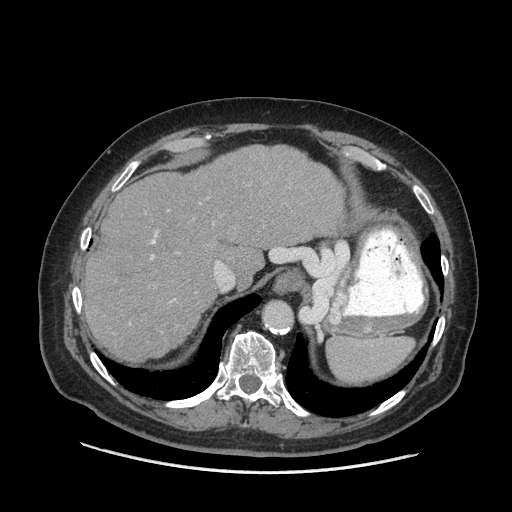
Contrast-enhanced abdominal CT (liver protocol), one axial slice. Soft-tissue window (W 400 / L 40 HU). 2.5 mm slice thickness. 512 × 512 image matrix, field of view 420 × 420 mm. Case-level facts recorded for this patient, not image findings: diagnosis: hepatocellular carcinoma (patient treated with transarterial chemoembolisation; whether this scan precedes or follows treatment is not stated here); TNM stage (as recorded): Stage-I; Child-Pugh class: A; tumour nodularity: uninodular; tumour size: 3.8 cm.
Outlined on this slice (semi-automatic segmentation, software-assisted and operator-edited):
- abdominal aorta: bounding box [x1, y1, x2, y2] px = [264, 302, 291, 327]
- liver parenchyma outside the tumour (the mass and vessels are separate outlines, so this box may not span the whole liver): [84, 146, 344, 360]
- liver vessels: [130, 232, 175, 325]